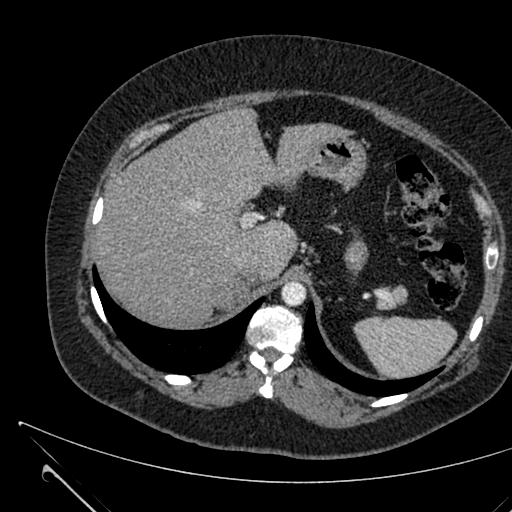
Contrast-enhanced abdominal CT, one axial slice. Position 486 of 731 along the scan axis. 120 kVp. Intravenous contrast given. Soft-tissue window (W 400 / L 40 HU). 1 mm slice thickness. 512 × 512 image matrix. Patient: female, 36 years. From the clinical record (not read from this slice): diagnosis: adrenocortical carcinoma; tumour side: right adrenal; tumour size at pathology: 10 cm; Ki-67 index: 20 %; stage (as recorded): 4.
Outlined on this slice (semi-automatically segmented with operator editing):
- mass: box from (x=215, y=282) to (x=246, y=308) px